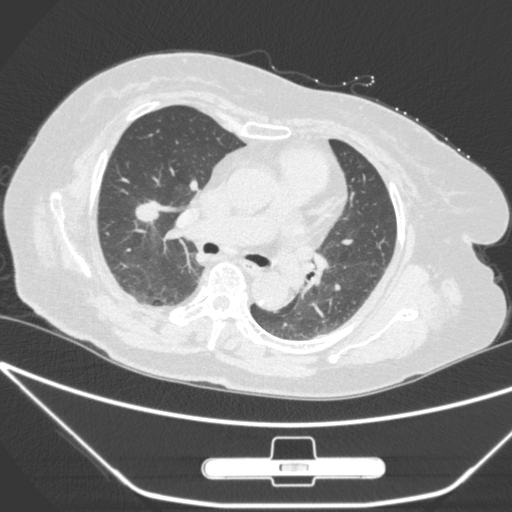
Chest CT, one axial slice; position 158 of 245 along the scan axis; lung window (W 1500 / L -600 HU); 1 mm slice thickness; 512 × 512 image matrix, field of view 365 × 365 mm. Patient: female, 65 years. From the clinical record (not read from this slice): clinical TNM (as recorded): T1c N0 M0.
Annotated regions visible in this slice (bounding box drawn by a radiologist):
- lung tumour (recorded histology: adenocarcinoma): bounding box [x1, y1, x2, y2] px = [128, 194, 176, 238]